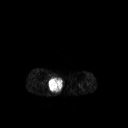
FDG PET of an extremity soft-tissue mass (from a PET/CT study), one axial slice. Slice 139 of 267 in the series (ordered by position). 3.27 mm slice thickness. 128 × 128 image matrix, field of view 500 × 500 mm. Patient: male, 69 years. Case-level facts recorded for this patient, not image findings: histological type: pleiomorphic liposarcoma; grade: high; site of the primary tumour: right calf.
Annotated regions visible in this slice (expert contour drawn on MRI and transferred to this co-registered scan by the dataset authors):
- gross tumour volume including surrounding oedema: bounding box [x1, y1, x2, y2] px = [48, 76, 63, 92]
- gross tumour volume (mass): [48, 76, 63, 91]